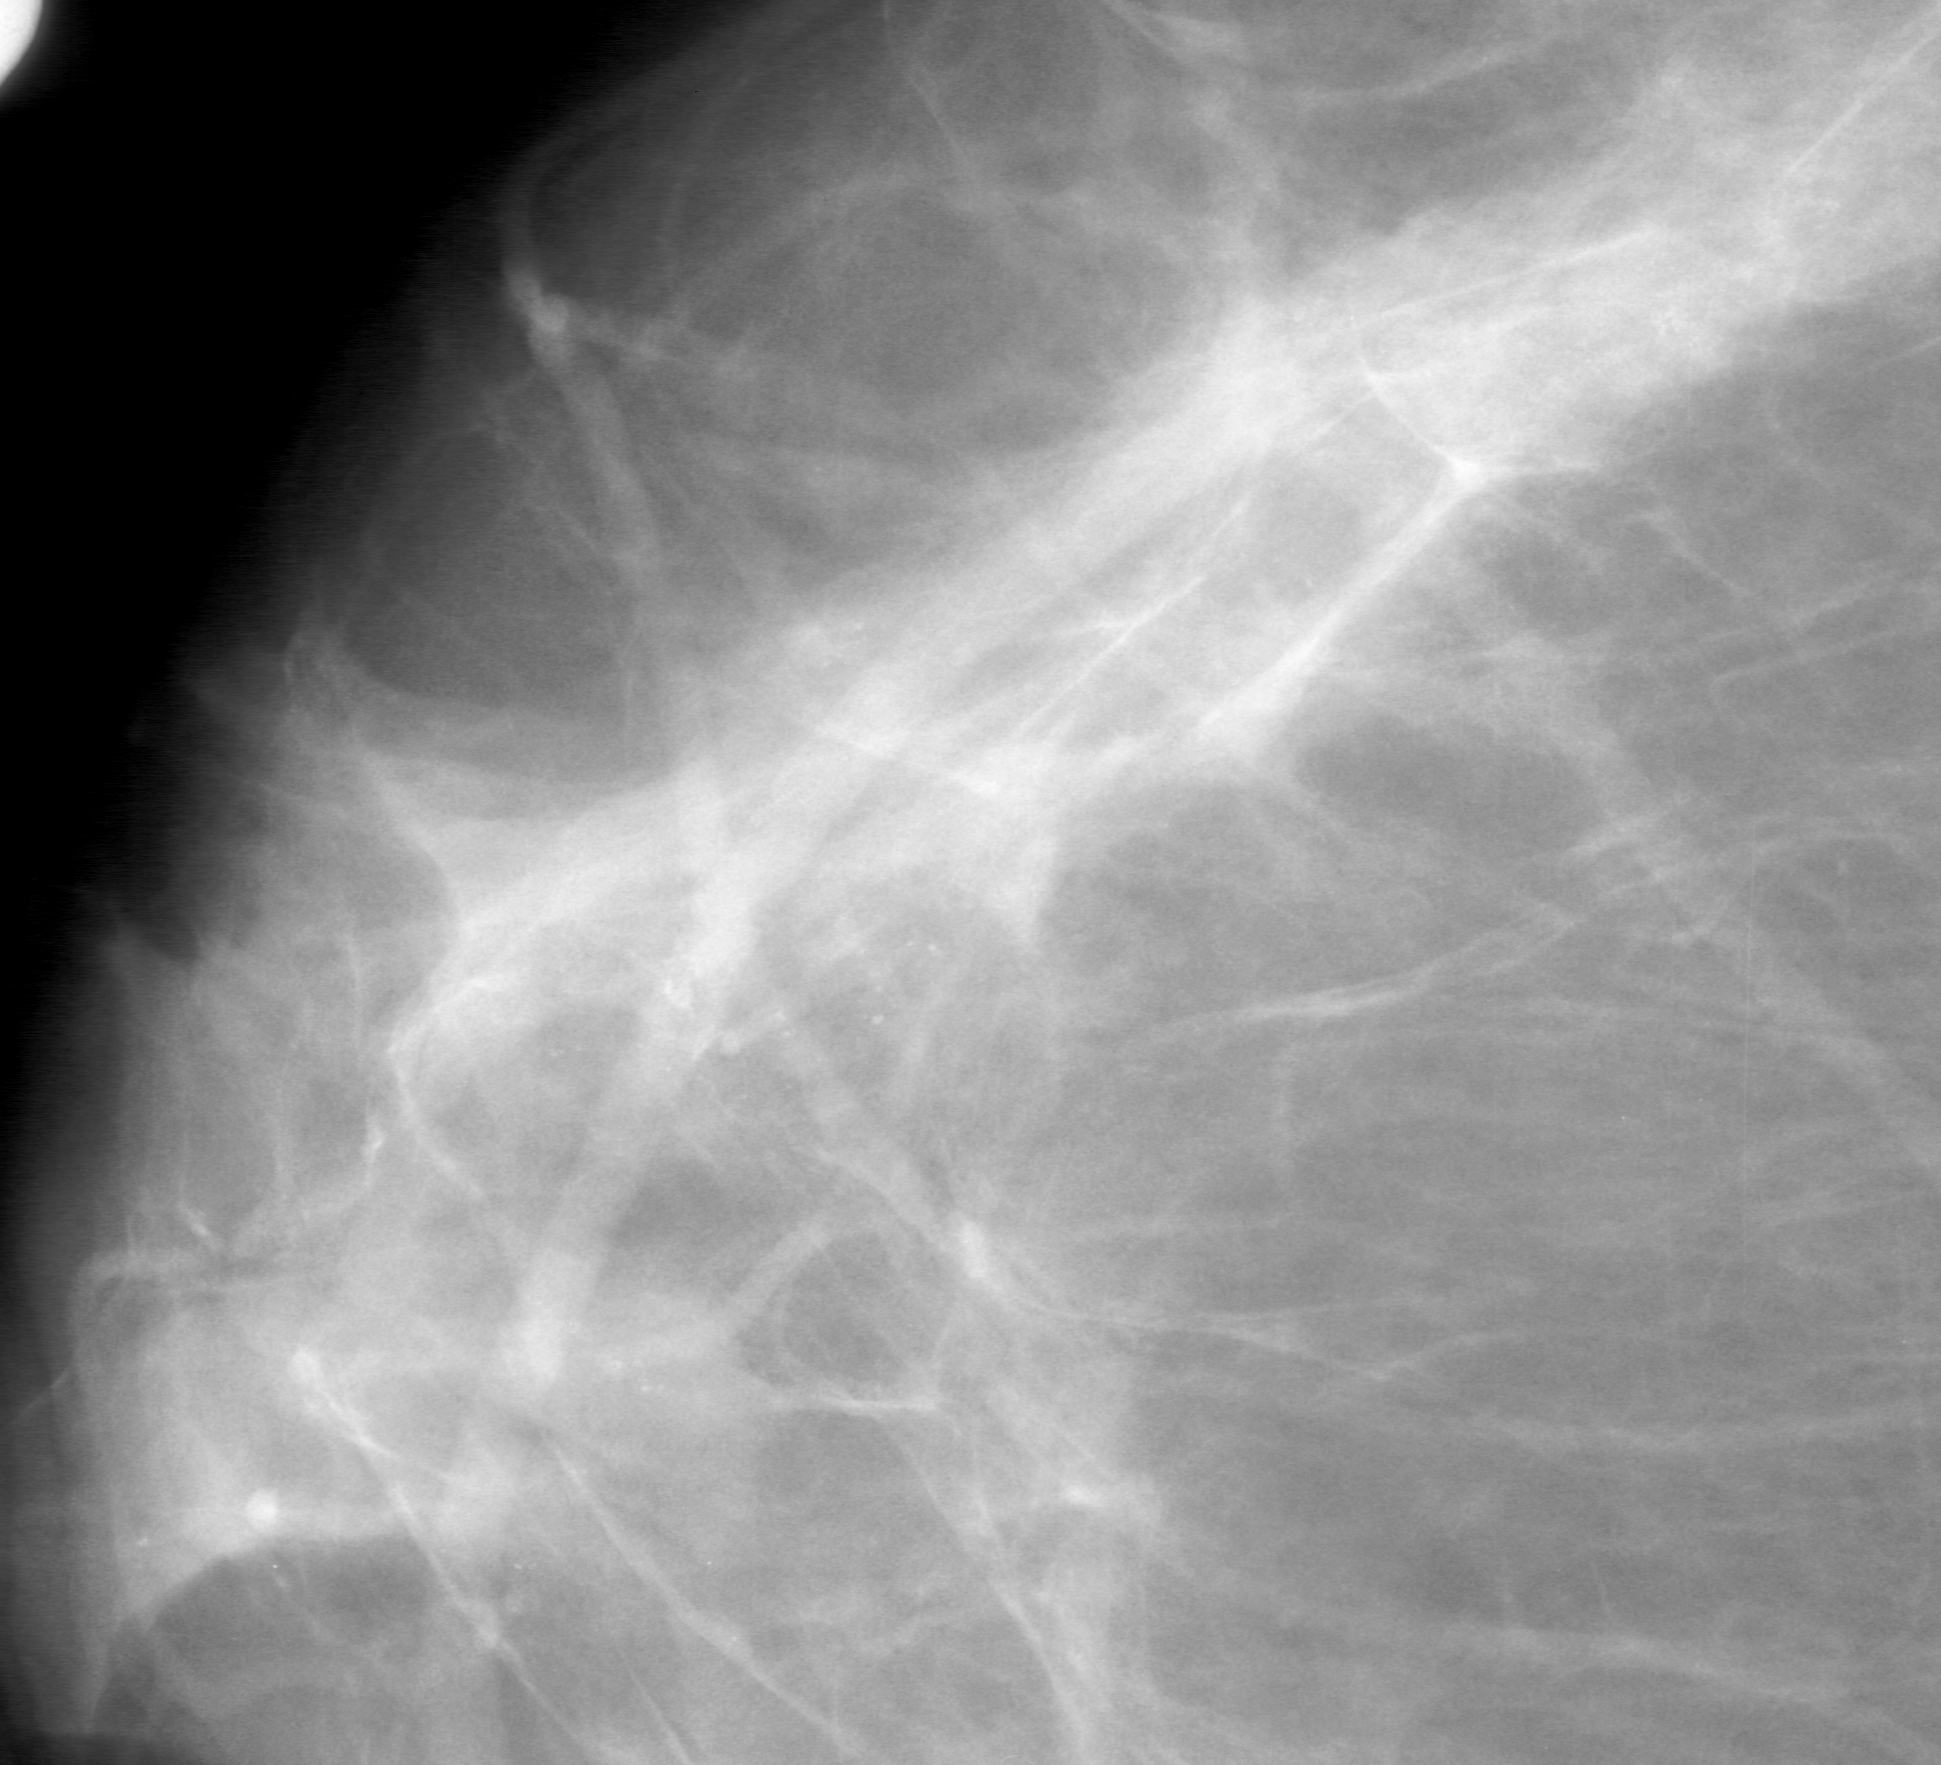
Region of interest cut from a scanned film mammogram (one marked finding); right breast; CC view.
Finding: calcifications, morphology amorphous, distribution segmental; BI-RADS assessment category 0 (incomplete: needs additional imaging); pathology result (as recorded, not read from the image): malignant.